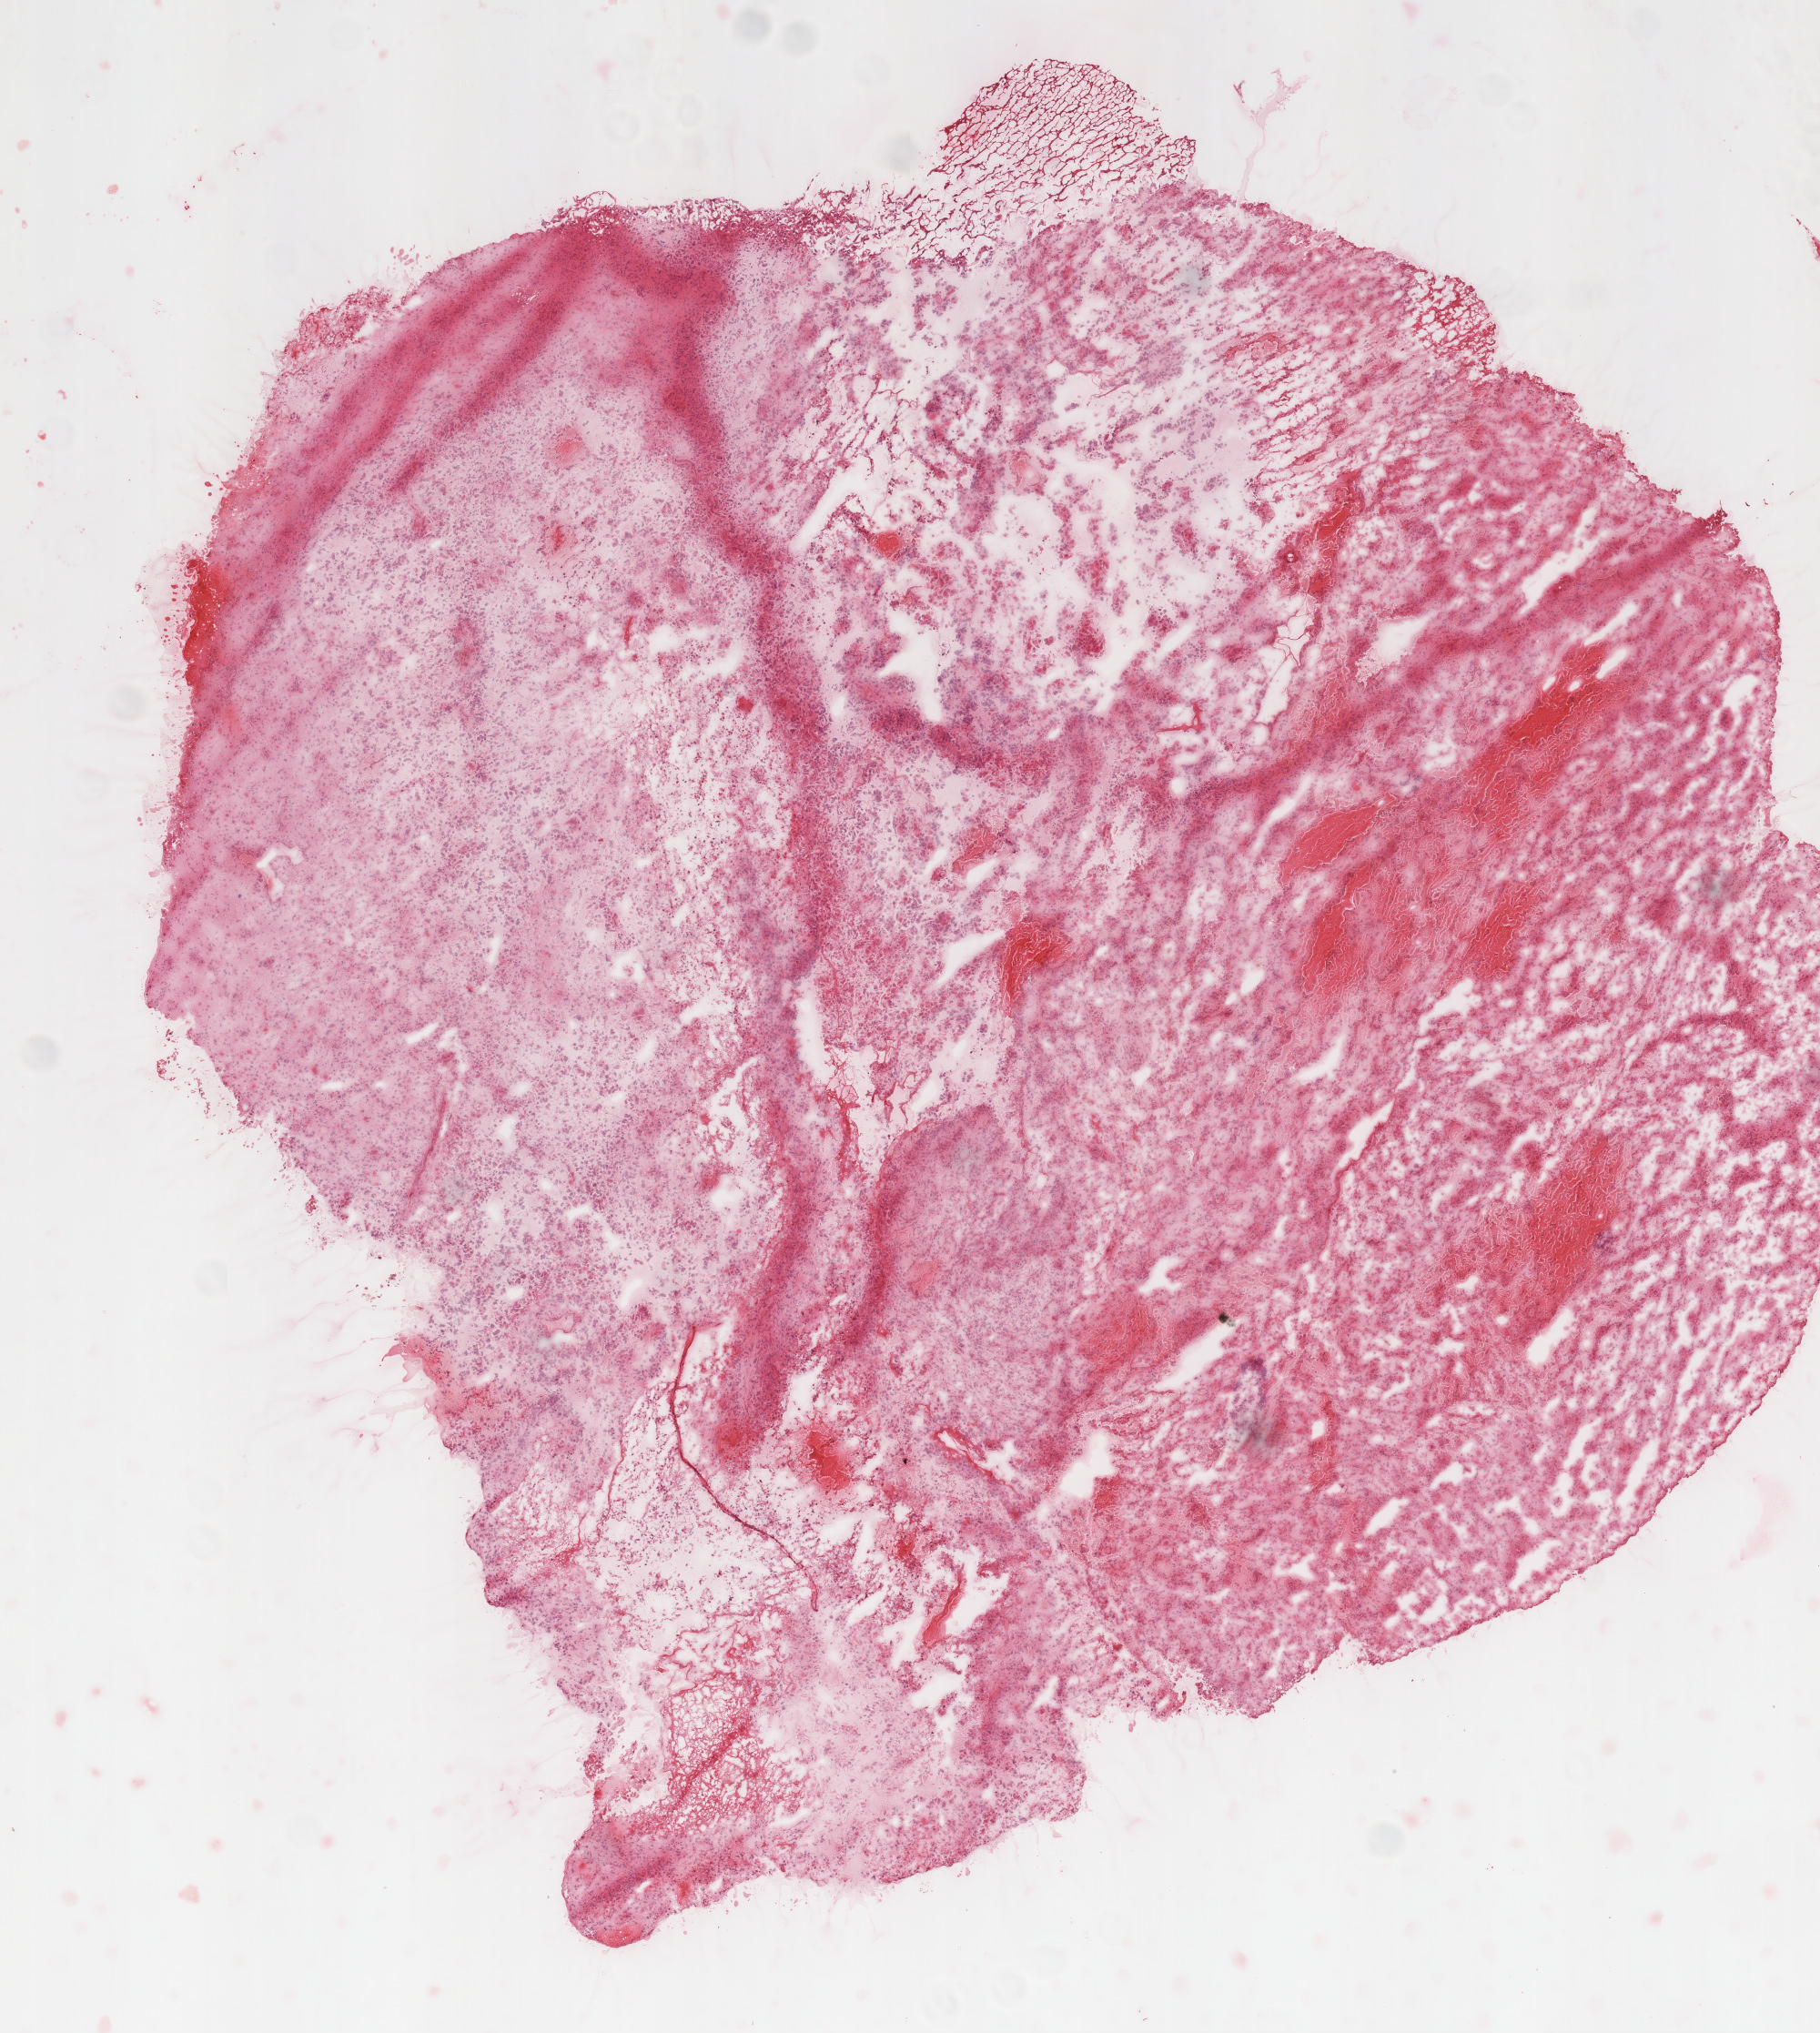
H&E-stained whole-slide image — a low-resolution overview of the entire scanned area, about 8.0 x 9.0 mm (acquisition: 20x scan); frozen section; brain, primary tumour sample. Male, age 58 years at initial diagnosis. Pathologist review of this section (percent, as recorded): tumour cells 80%, tumour nuclei 80%, normal cells 0%, stromal cells 5%, necrosis 15%.
* diagnosis: Glioblastoma